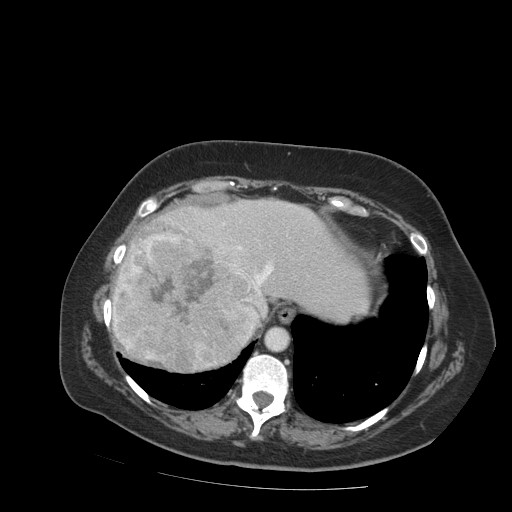
Contrast-enhanced abdominal CT (liver protocol), one axial slice. Position 72 of 99 along the scan axis. Reconstruction kernel STANDARD. 140 kVp. Soft-tissue window (W 400 / L 40 HU). 2.5 mm slice thickness. 512 × 512 image matrix. Case-level facts recorded for this patient, not image findings: diagnosis: hepatocellular carcinoma (patient treated with transarterial chemoembolisation; whether this scan precedes or follows treatment is not stated here); TNM stage (as recorded): Stage-IVB; Child-Pugh class: A; tumour nodularity: uninodular.
Annotated regions visible in this slice (semi-automatic segmentation, software-assisted and operator-edited):
- abdominal aorta: bounding box [x1, y1, x2, y2] px = [266, 328, 288, 350]
- liver parenchyma outside the tumour (the mass and vessels are separate outlines, so this box may not span the whole liver): [112, 200, 370, 368]
- mass: [110, 229, 266, 373]
- liver vessels: [222, 223, 274, 328]